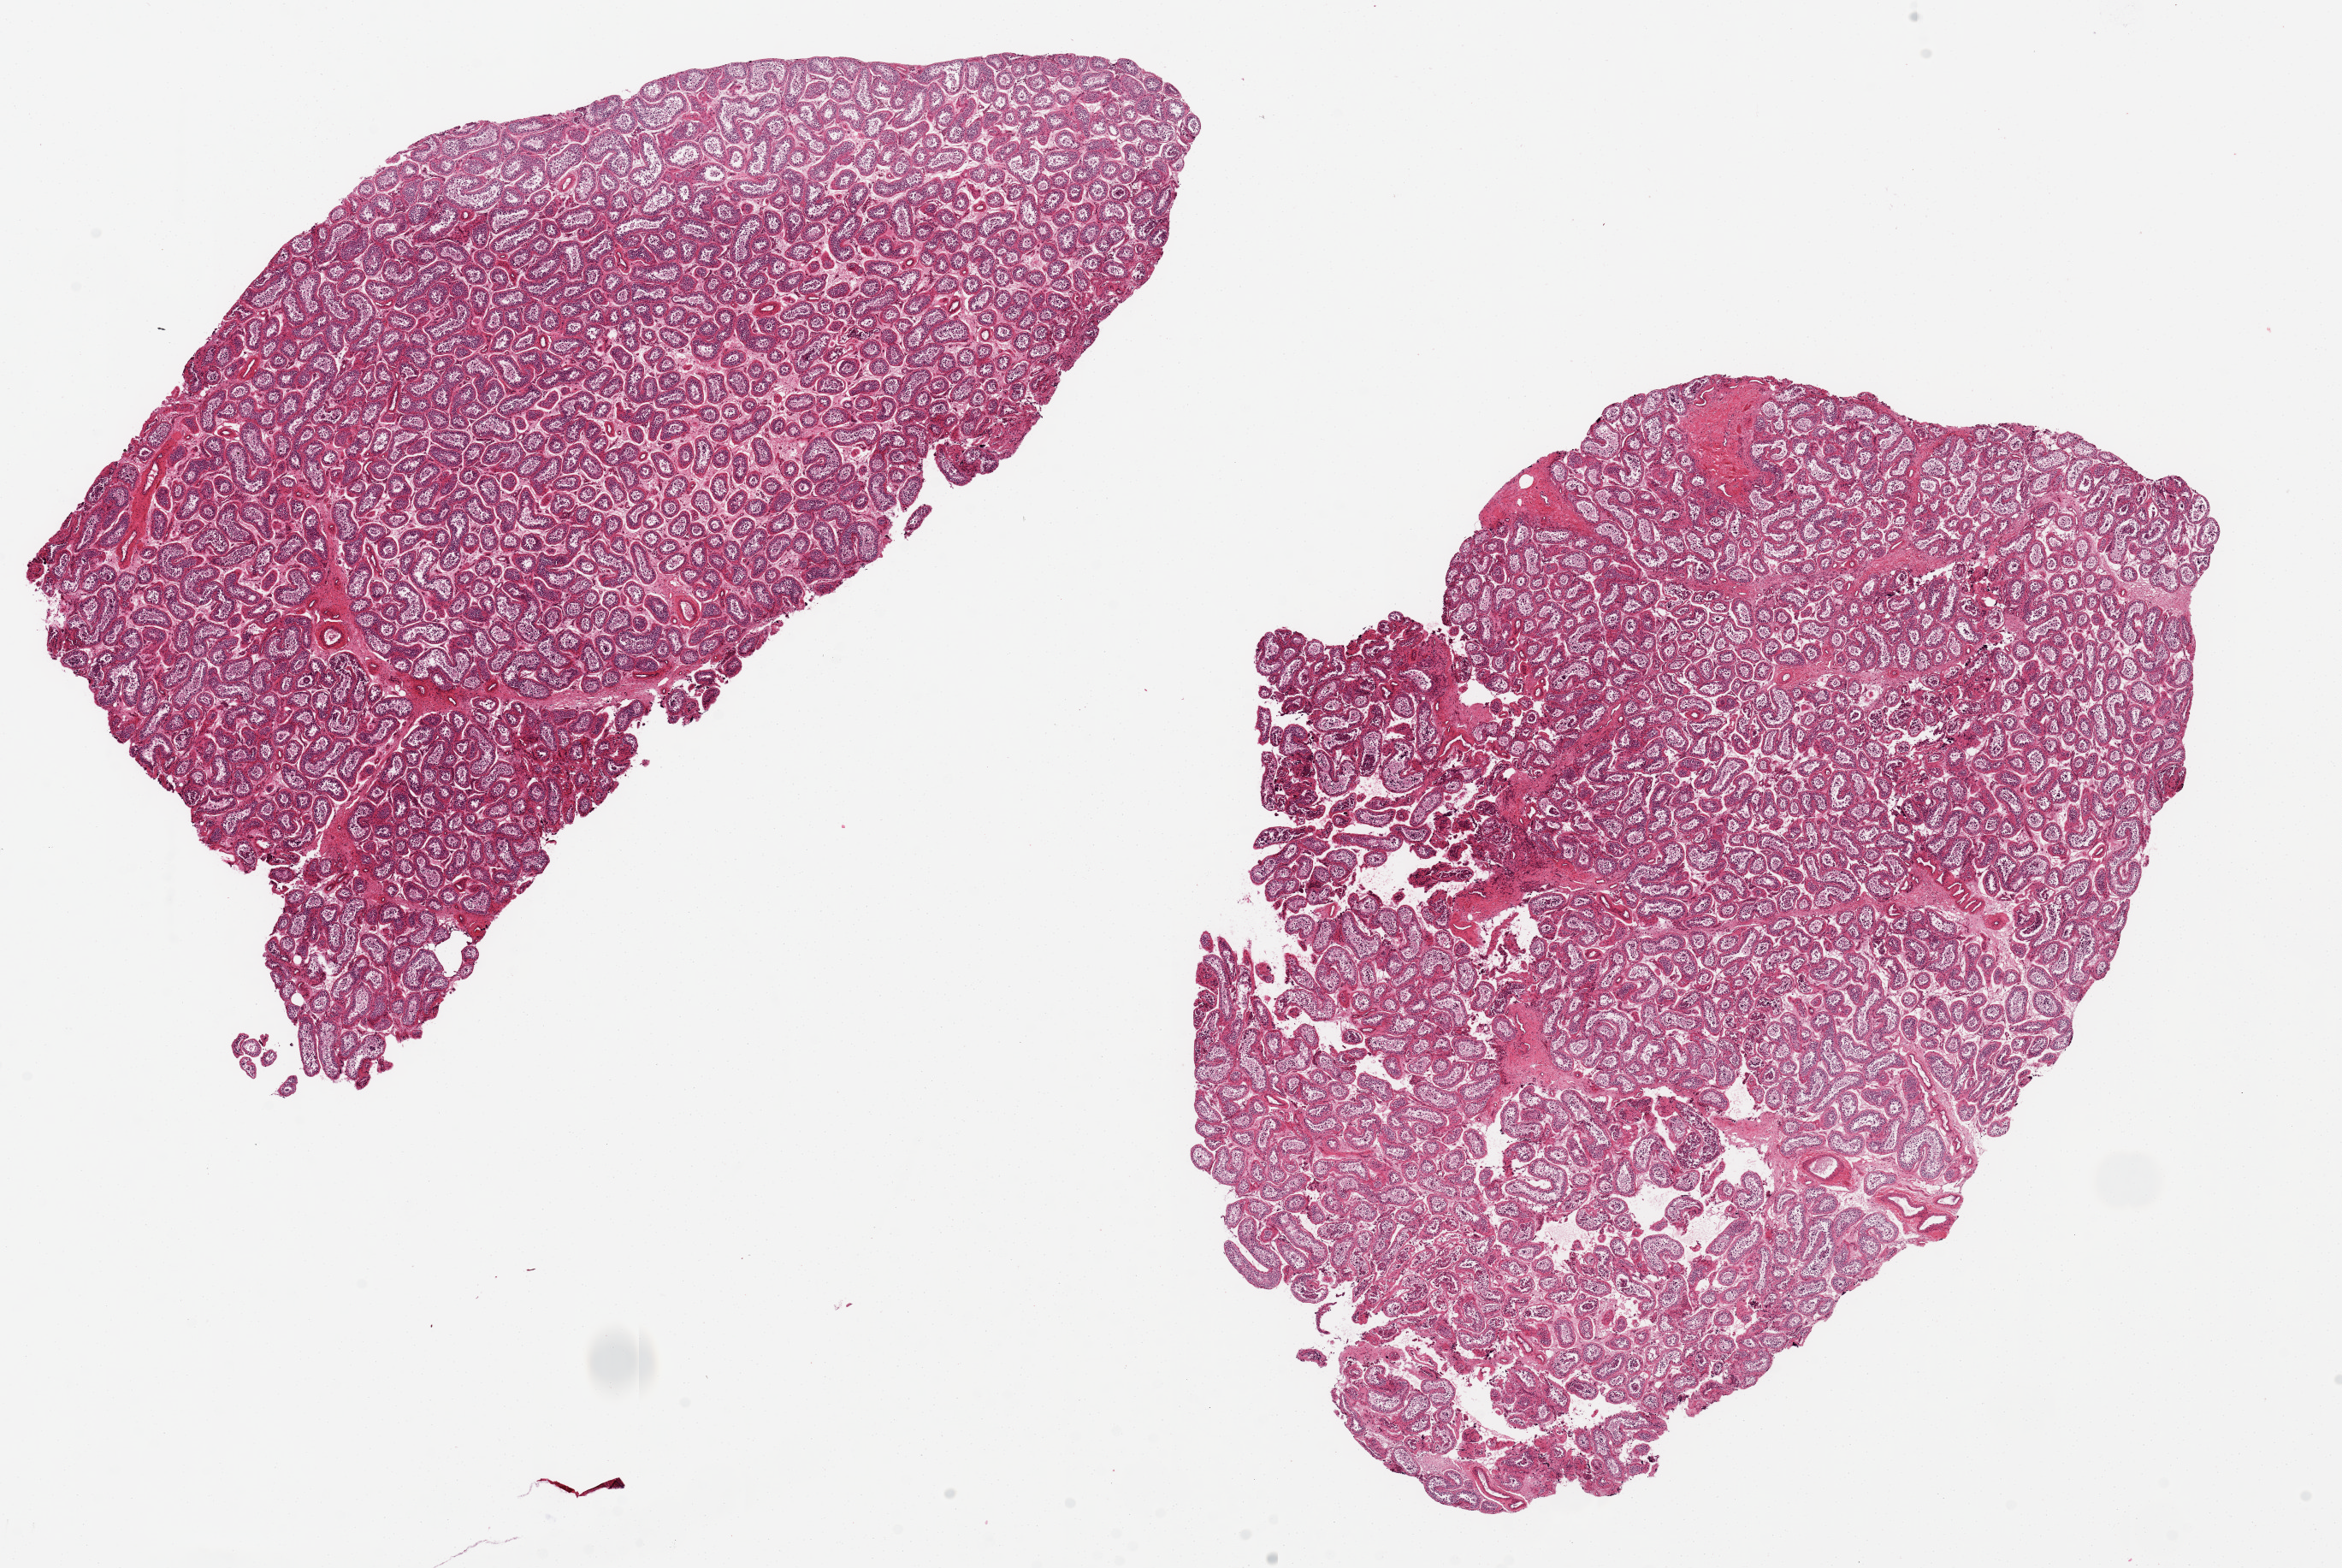
Digitized H&E-stained section, brightfield — whole scanned area (about 21.7 x 14.5 mm) shown as a low-resolution overview; PAXgene-fixed paraffin-embedded (PFPE) section; sampled site (target tissue): testis; donor tissue sample. Donor: male.
- reviewer comment on this tissue sample: 2 pieces 12x5&12x8 mm; reduced spermatogenesis